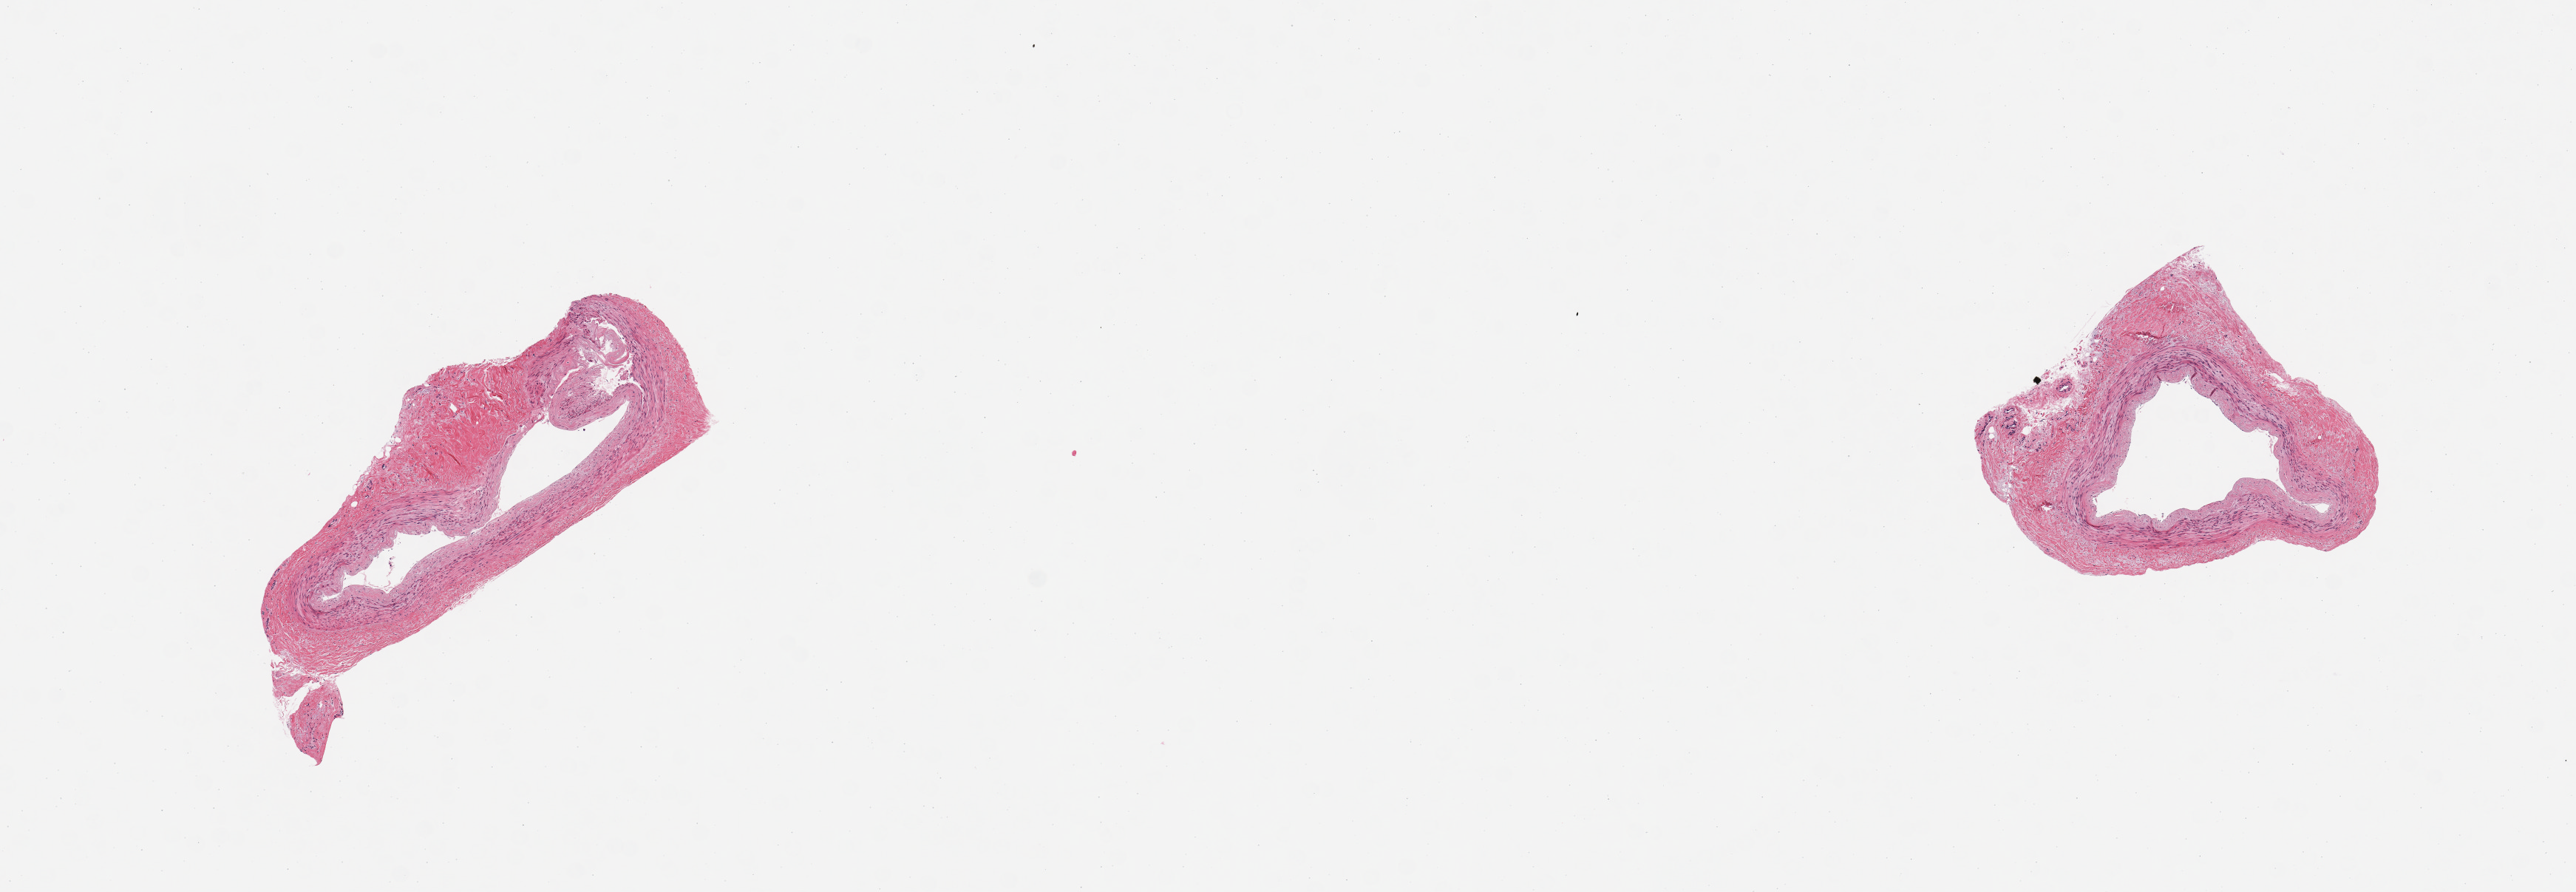
Hematoxylin and eosin (H&E) whole-slide image, brightfield — low-resolution overview of the scanned area, about 13.8 x 4.8 mm; PAXgene-fixed, paraffin-embedded tissue; section of tibial artery (target tissue); donor tissue sample. Male donor.
Reviewer comment on this tissue sample: 2 pieces; mild plaque; well trimmed.